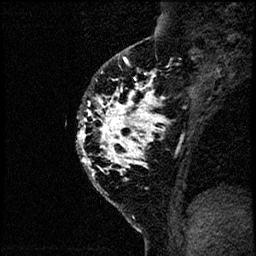
Breast MRI (dynamic contrast-enhanced), one sagittal slice; position 45 of 60 along the scan axis; dynamic contrast-enhanced study with each time point stored as its own series, time point 2 of 4 at this slice position (early post-contrast, ordered by acquisition time); 1.5 T; TE 4.2 ms, TR 17.6 ms; 2 mm slice thickness; 256 × 256 image matrix, field of view 200 × 200 mm. Patient: female, 40 years. From the clinical record (not read from this slice): setting: breast cancer imaged before/during neoadjuvant chemotherapy; receptor status: HER2-positive.
Structures marked on this image (semi-automatically segmented with operator editing):
- analysis volume of interest (the breast-tissue region the enhancement analysis was run in; not a lesion): bounding box [x1, y1, x2, y2] px = [72, 55, 185, 206]
- tumour enhancement mask (voxels above the 100 % enhancement threshold inside the analysis volume of interest): [76, 57, 185, 170]